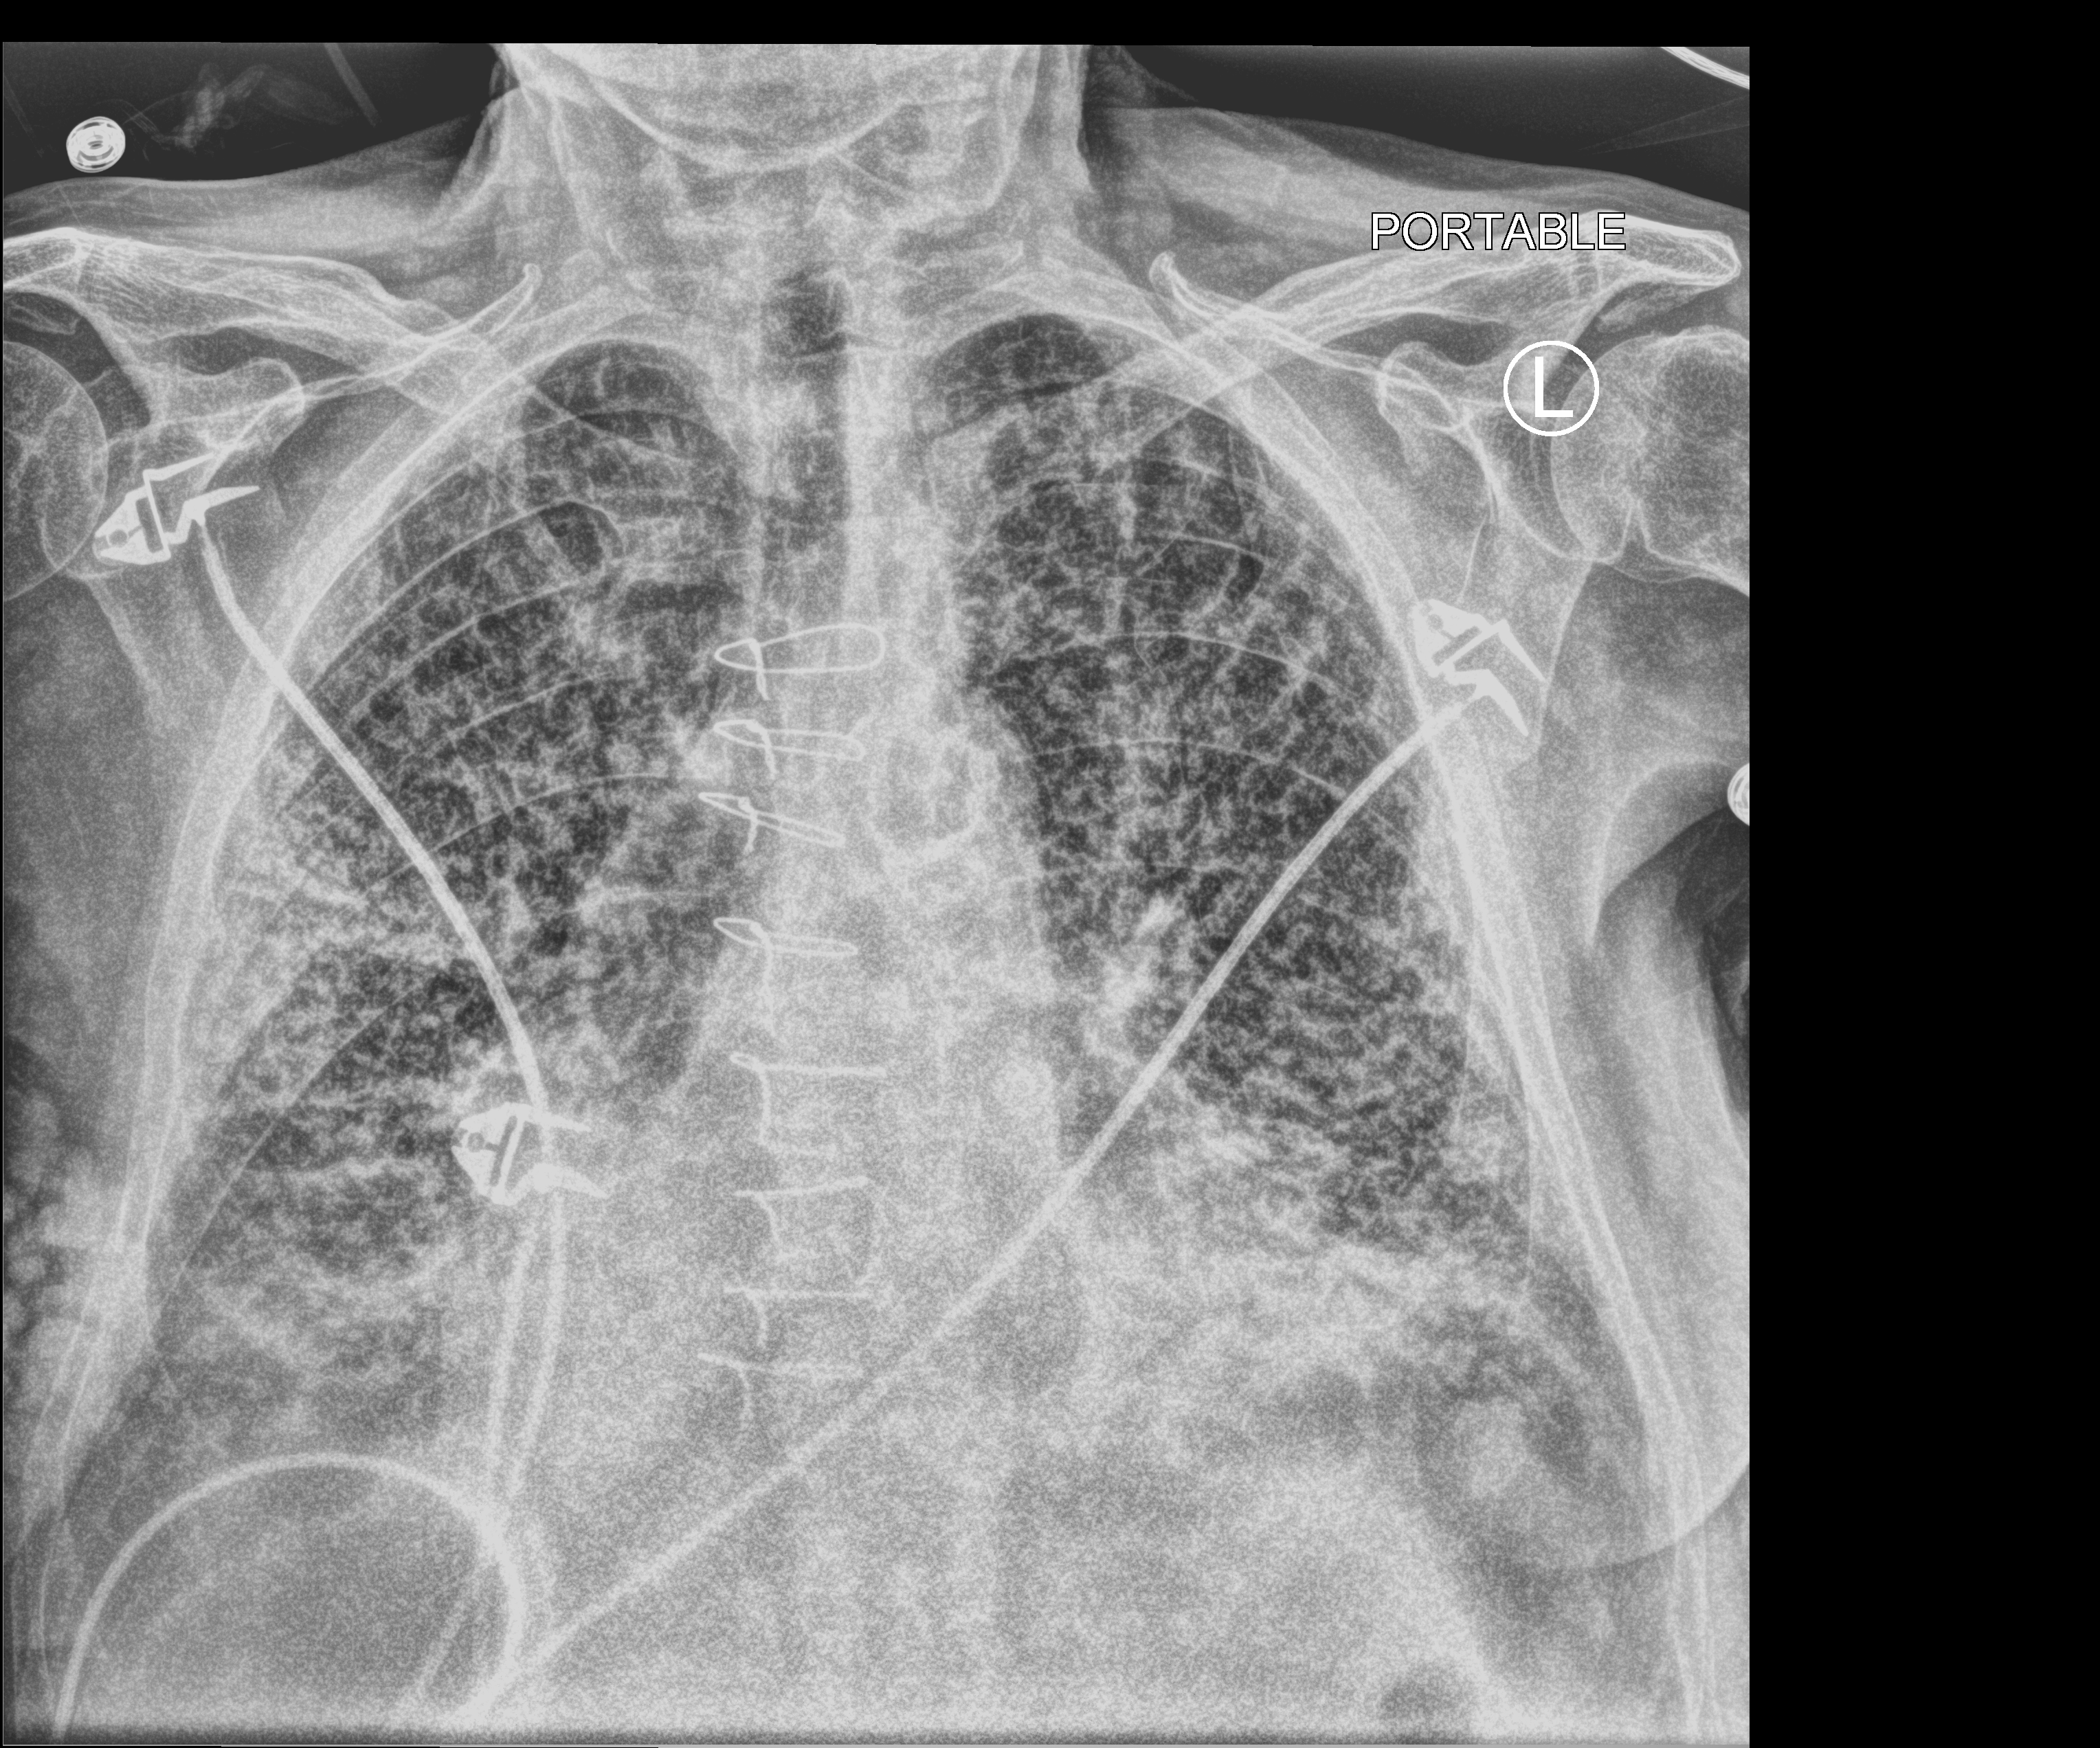
Bedside chest radiograph (computed radiography), anteroposterior (AP) projection. Male patient hospitalised with COVID-19, age 75–90 years.
Hospital-stay facts (about this admission, not read from this image; timing relative to this image not recorded): admitted to intensive care during this hospital stay: yes; mechanically ventilated during this hospital stay: yes.